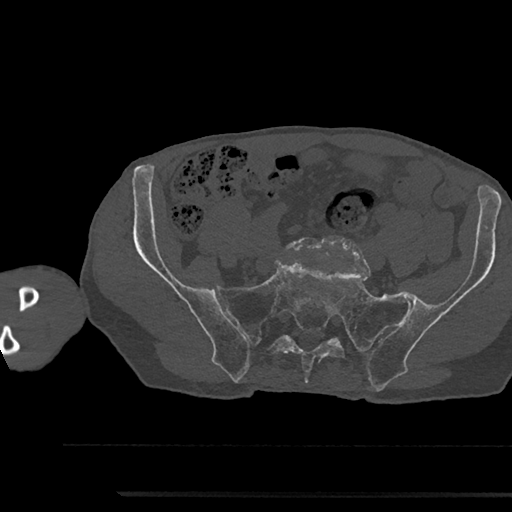
CT including the spine, one axial slice; slice 285 of 797 in the series (ordered by position); reconstruction kernel Br40s/3; 120 kVp; bone window (W 1800 / L 400 HU); 0.5 mm slice thickness; 512 × 512 image matrix. Patient: male, 79 years. From the clinical record (not read from this slice): primary cancer: prostate.
Annotated regions visible in this slice (semi-automatic segmentation, software-assisted and operator-edited):
- L5 vertebra: box from (x=286, y=238) to (x=353, y=252) px